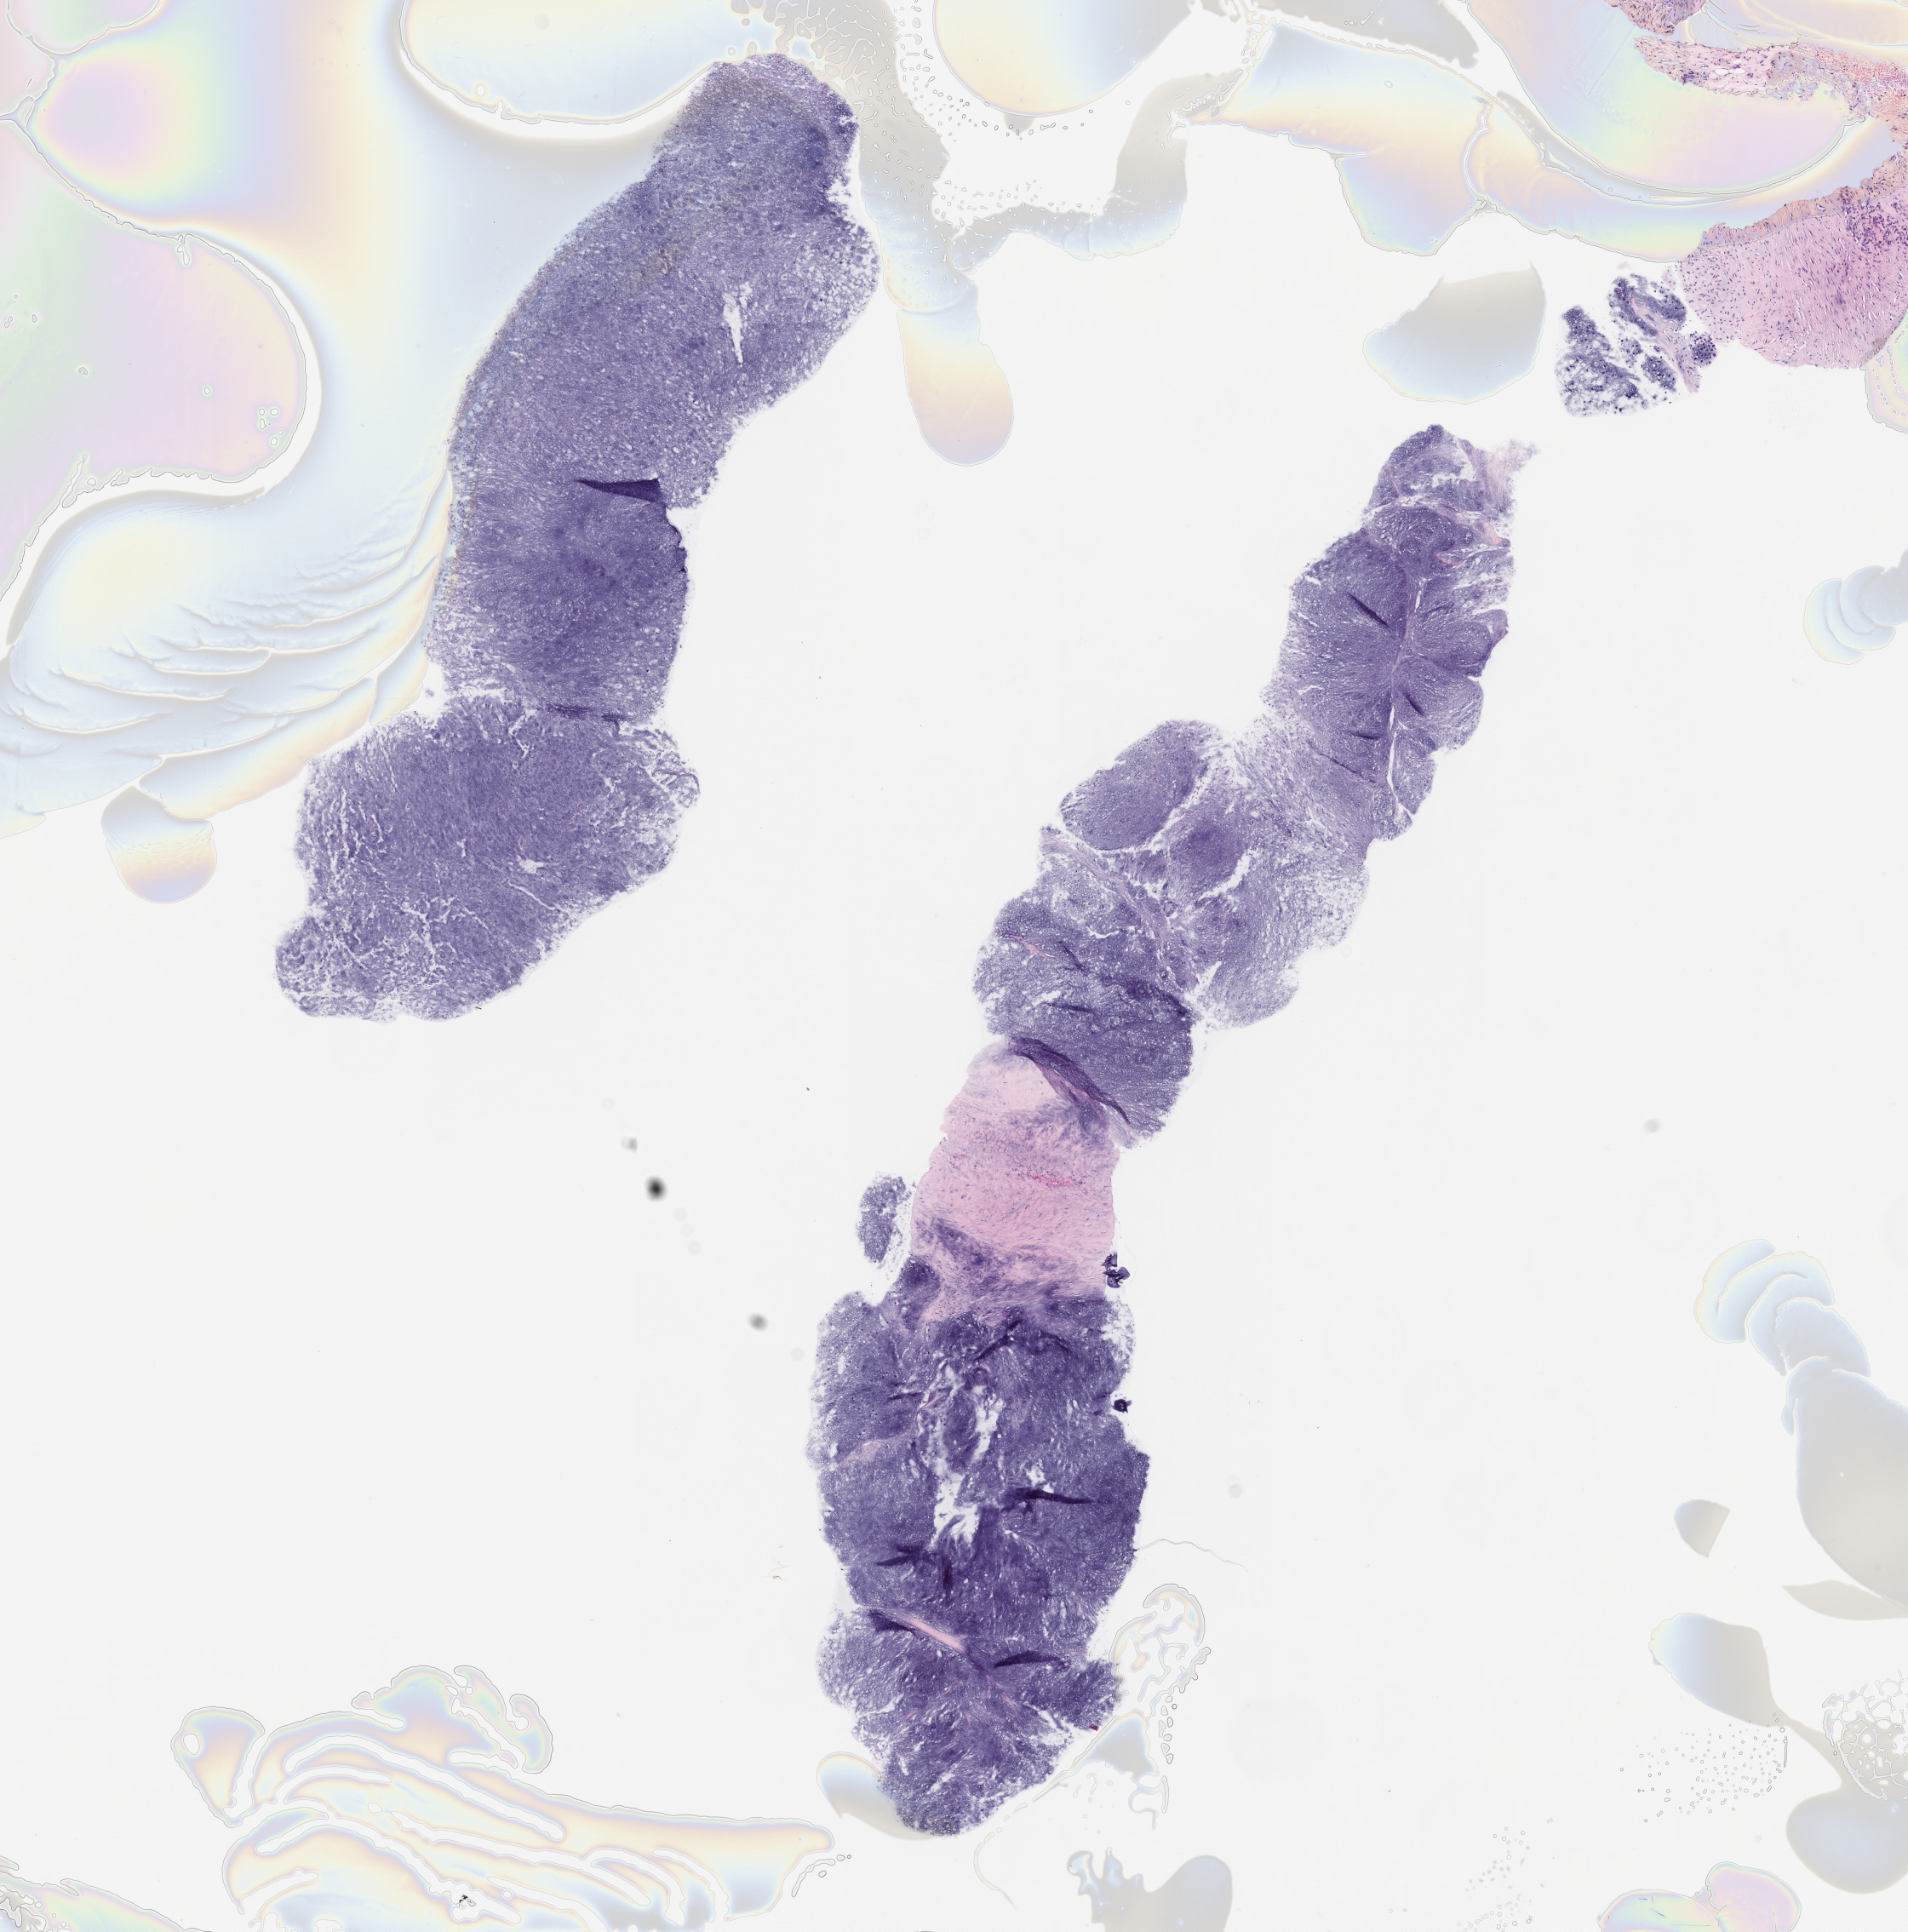
Haematoxylin and eosin whole-slide image of the patient's (originator) tumor tissue, shown as a low-resolution overview of the whole scanned area (about 9.0 x 9.1 mm). FFPE section. Tumor site category: musculoskeletal. Patient male; aged 60.
Diagnosis: Chondrosarcoma.